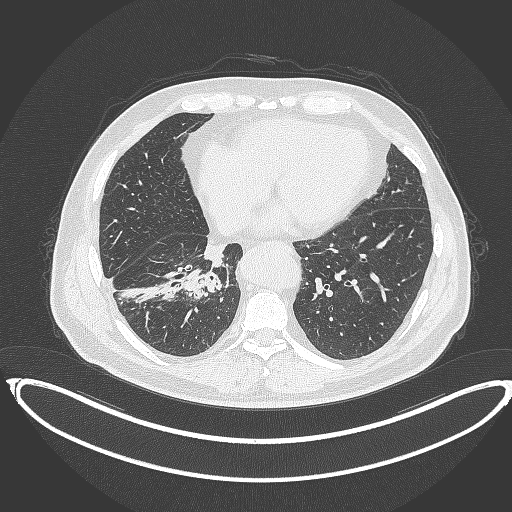
Chest CT, one axial slice; slice 144 of 387 in the series (ordered by position); reconstruction kernel B70f; lung window (W 1500 / L -600 HU); 1 mm slice thickness; 512 × 512 image matrix, field of view 448 × 448 mm. Male patient, age 61 years. Case-level facts recorded for this patient, not image findings: clinical TNM (as recorded): T1b N1 M0.
Outlined on this slice (rectangle marked by the reading radiologist):
- lung tumour (recorded histology: squamous cell carcinoma): bounding box <180,267,222,300> (left, top, right, bottom; pixels)